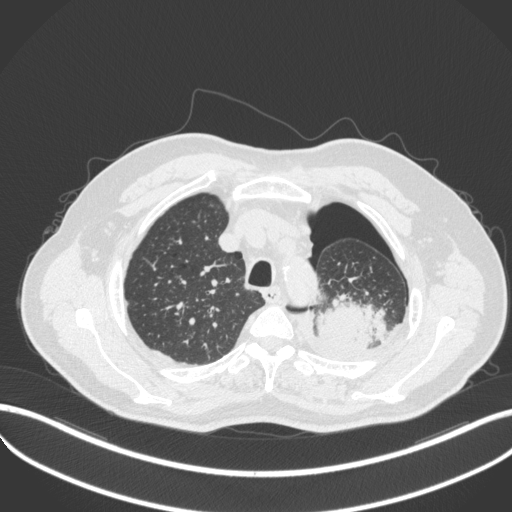
Chest CT, one axial slice; slice 405 of 466 in the series (ordered by position); reconstruction kernel B31f; lung window (W 1500 / L -600 HU); 1 mm slice thickness; 512 × 512 image matrix, field of view 400 × 400 mm. Male patient, age 76 years. From the clinical record (not read from this slice): clinical TNM (as recorded): T3 N0 M1b.
Structures marked on this image (bounding box drawn by a radiologist):
- lung tumour (recorded histology: adenocarcinoma): box from (x=310, y=296) to (x=388, y=355) px